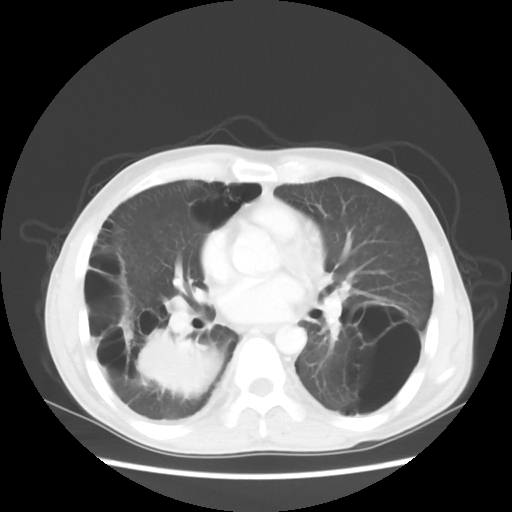
Chest CT, one axial slice; position 26 of 56 along the scan axis; lung window (W 1500 / L -600 HU); 5 mm slice thickness; 512 × 512 image matrix. Patient: male, 41 years. Case-level facts recorded for this patient, not image findings: clinical TNM (as recorded): T4 N0 M1a.
Outlined on this slice (rectangle marked by the reading radiologist):
- lung tumour (recorded histology: large cell carcinoma): bounding box (x1, y1, x2, y2) in pixels: (132, 327, 225, 400)